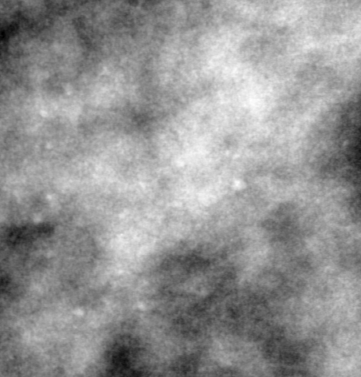
Region of interest cut from a scanned film mammogram (one marked finding), right breast, MLO view.
- Marked abnormality: calcifications, morphology pleomorphic, distribution clustered; BI-RADS assessment category 4; subtlety rating 2 on a 1 (subtle) to 5 (obvious) scale; pathology (as recorded): benign.